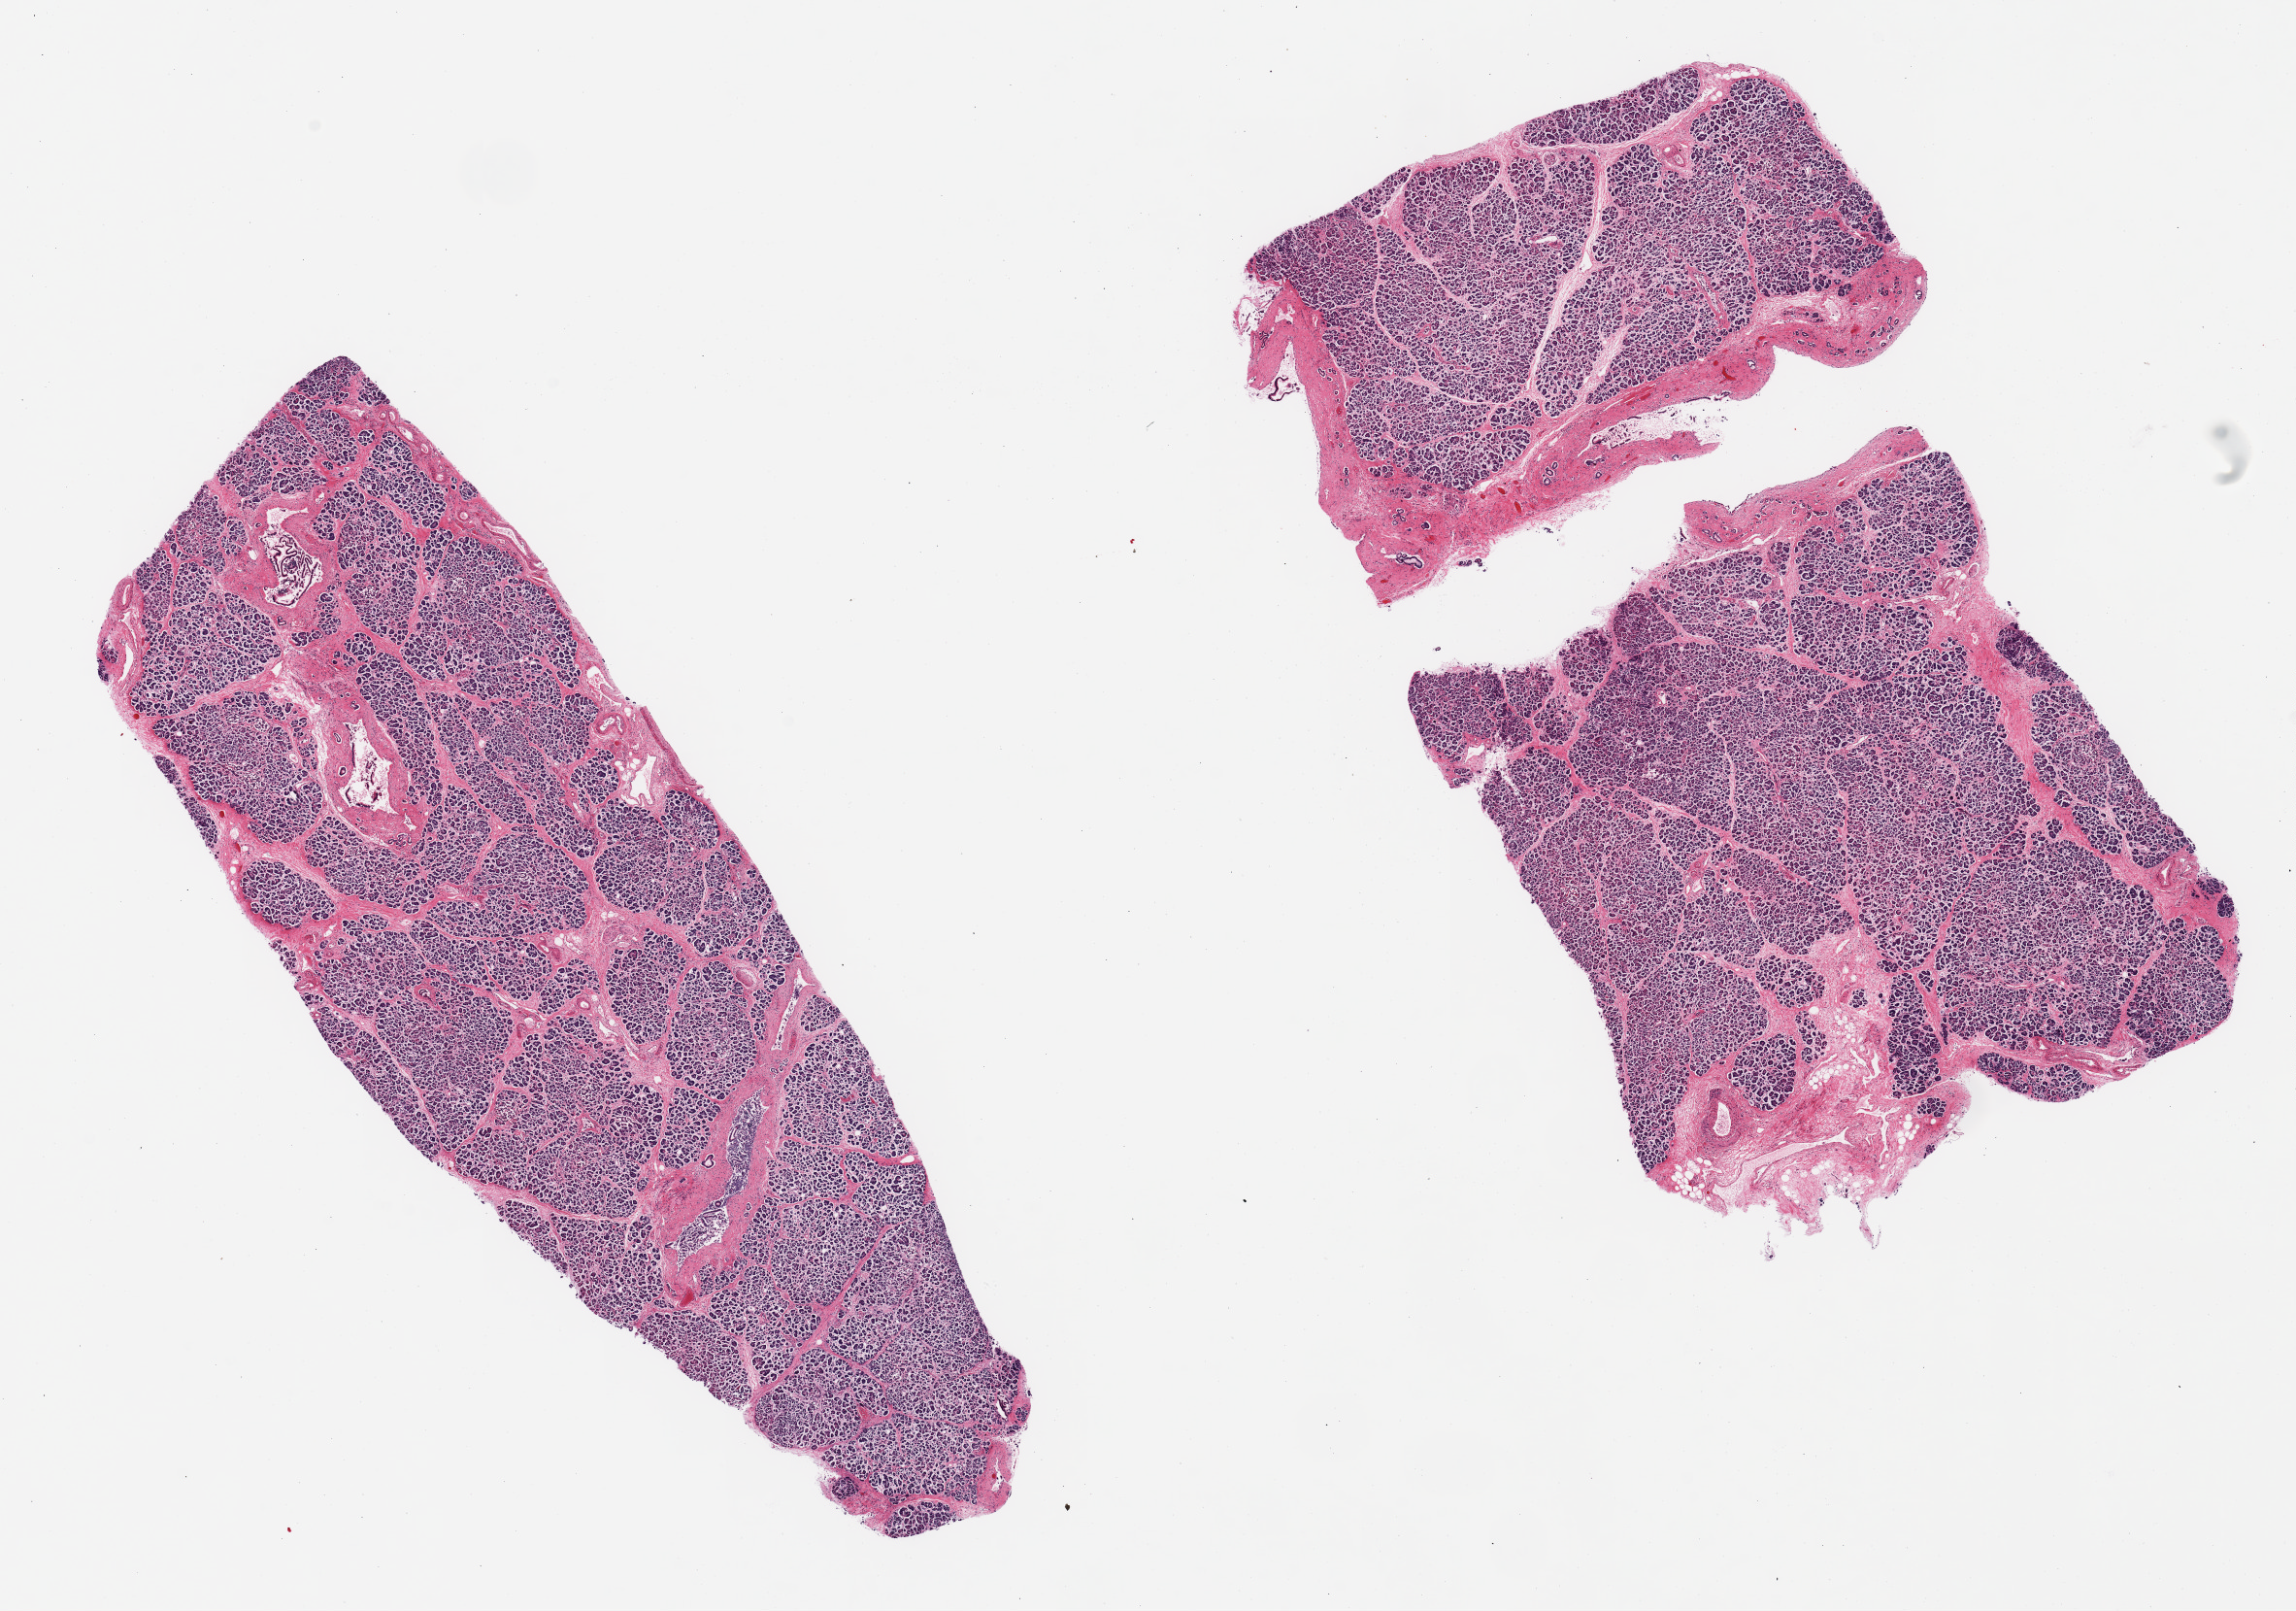
H&E whole-slide image, brightfield, whole scanned area (about 18.7 x 13.1 mm, acquisition: 20x scan) shown as a low-resolution overview. PAXgene-fixed paraffin-embedded (PFPE) section. Sampled site (target tissue): pancreas. Tissue donor sample. Female donor.
* review note (as recorded): 2 pieces; moderate fibrosis